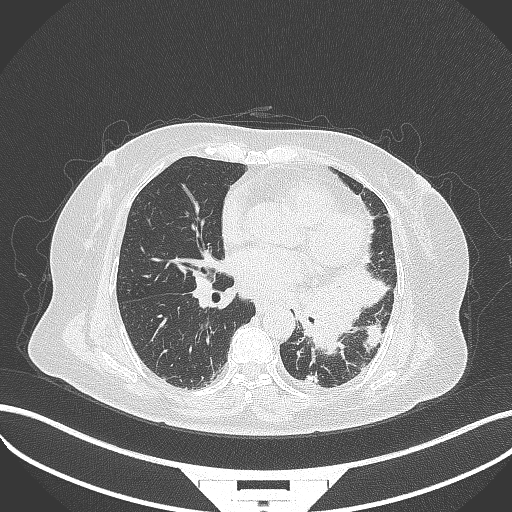
Chest CT, one axial slice. Slice 164 of 322 in the series (ordered by position). Reconstruction kernel B70f. Lung window (W 1500 / L -600 HU). 1 mm slice thickness. 512 × 512 image matrix. Patient: female, 69 years. Case-level facts recorded for this patient, not image findings: clinical TNM (as recorded): T2b N3 M1.
Structures marked on this image (rectangle marked by the reading radiologist):
- lung tumour (recorded histology: adenocarcinoma): bounding box [x1, y1, x2, y2] px = [292, 261, 390, 354]